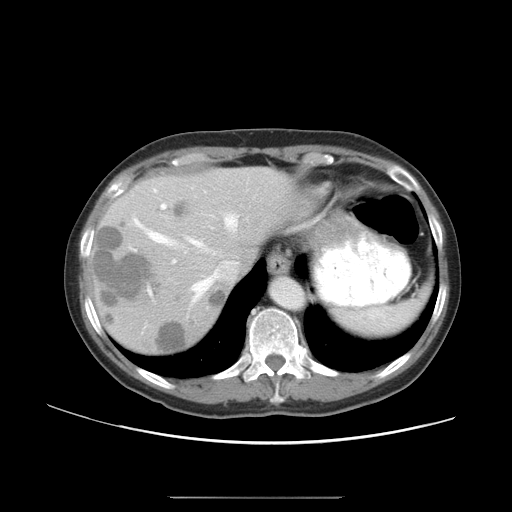
Contrast-enhanced abdominal CT, one axial slice. Slice 38 of 50 in the series (ordered by position). Reconstruction kernel STANDARD. 120 kVp. Soft-tissue window (W 400 / L 40 HU). 512 × 512 image matrix. Female patient, age 58 years. Case-level facts recorded for this patient, not image findings: diagnosis: colorectal cancer liver metastases, imaged before liver resection; multiple liver metastases: yes; largest metastasis: 7.3 cm.
Structures marked on this image (manually delineated by an expert):
- hepatic veins: bounding box [x1, y1, x2, y2] px = [135, 188, 237, 303]
- liver: [93, 170, 286, 354]
- planned liver remnant (the part of the liver to remain after resection): [186, 170, 286, 261]
- portal vein (with intrahepatic branches): [160, 190, 207, 262]
- liver metastasis: [155, 321, 188, 354]
- liver metastasis: [173, 204, 187, 219]
- liver metastasis: [211, 292, 228, 306]
- liver metastasis: [96, 219, 154, 325]